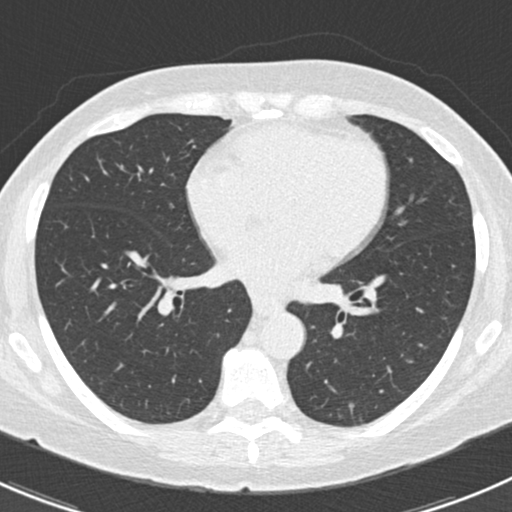
Axial slice from a low-dose chest CT screening exam, second annual screen, lung window (W 1500 / L -600 HU), standard (soft-tissue) reconstruction kernel (B30f), 120 kVp, slice 85 of 166 in the series. Female, age 64 years at enrolment. Former smoker at enrolment.
Expert-annotated lung lesion, bounding box (x1, y1, x2, y2) in pixels: (326, 390, 380, 436). Reader record for this screening exam (exam-level; its link to the box is not recorded): non-calcified nodule or mass ≥4 mm, left lower lobe, 8 × 3 mm, poorly defined margins, soft tissue attenuation, pre-existing on the prior screen: yes; interval growth: no.